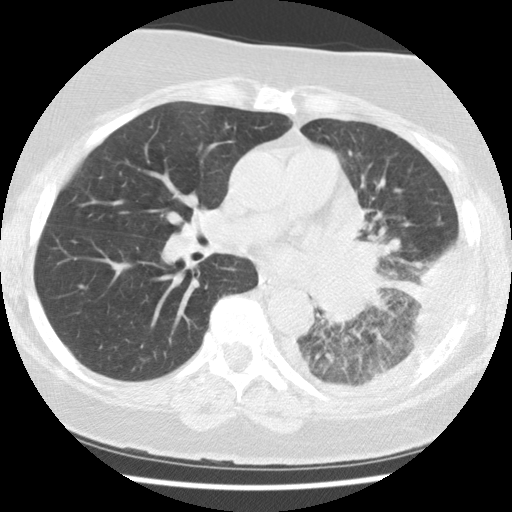
Chest CT (low-dose screening protocol), one axial image; baseline annual screen; lung window (W 1500 / L -600 HU); 2.5 mm slice thickness; standard (soft-tissue) reconstruction kernel (STANDARD); 120 kVp; slice 56 of 114 in the series. Female participant, aged 65 years at enrolment. Current smoker at enrolment.
Expert-annotated lung lesion, box from (x=299, y=283) to (x=400, y=362) px. Screening reader's record for this exam (one nodule recorded; not confirmed to be the boxed lesion): non-calcified nodule or mass ≥4 mm, left lower lobe, 74 × 48 mm, spiculated (stellate) margins, soft tissue attenuation. Official screen result: positive, change unspecified: nodule(s) >= 4 mm or enlarging nodule(s), mass(es), or other non-specific abnormalities suspicious for lung cancer. Lung cancer was diagnosed 13 days after this screen: adenocarcinoma, NOS, left lower lobe, stage IV (AJCC 6th edition), 74 mm at pathology.